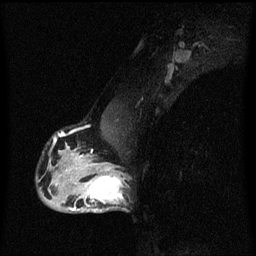
Breast MRI (dynamic contrast-enhanced), one sagittal slice. Position 39 of 60 along the scan axis. Dynamic contrast-enhanced series, image 2 of 3 at this slice position (ordered by acquisition). 1.5 T. TE 4.2 ms, TR 8.4 ms. 256 × 256 image matrix, field of view 200 × 200 mm. Female patient, age 40 years.
Structures marked on this image (semi-automatically segmented with operator editing):
- analysis volume of interest (the breast-tissue region the enhancement analysis was run in; not a lesion): bounding box [x1, y1, x2, y2] px = [76, 172, 128, 213]
- tumour enhancement mask (voxels above the 70 % enhancement threshold inside the analysis volume of interest): [76, 172, 124, 211]